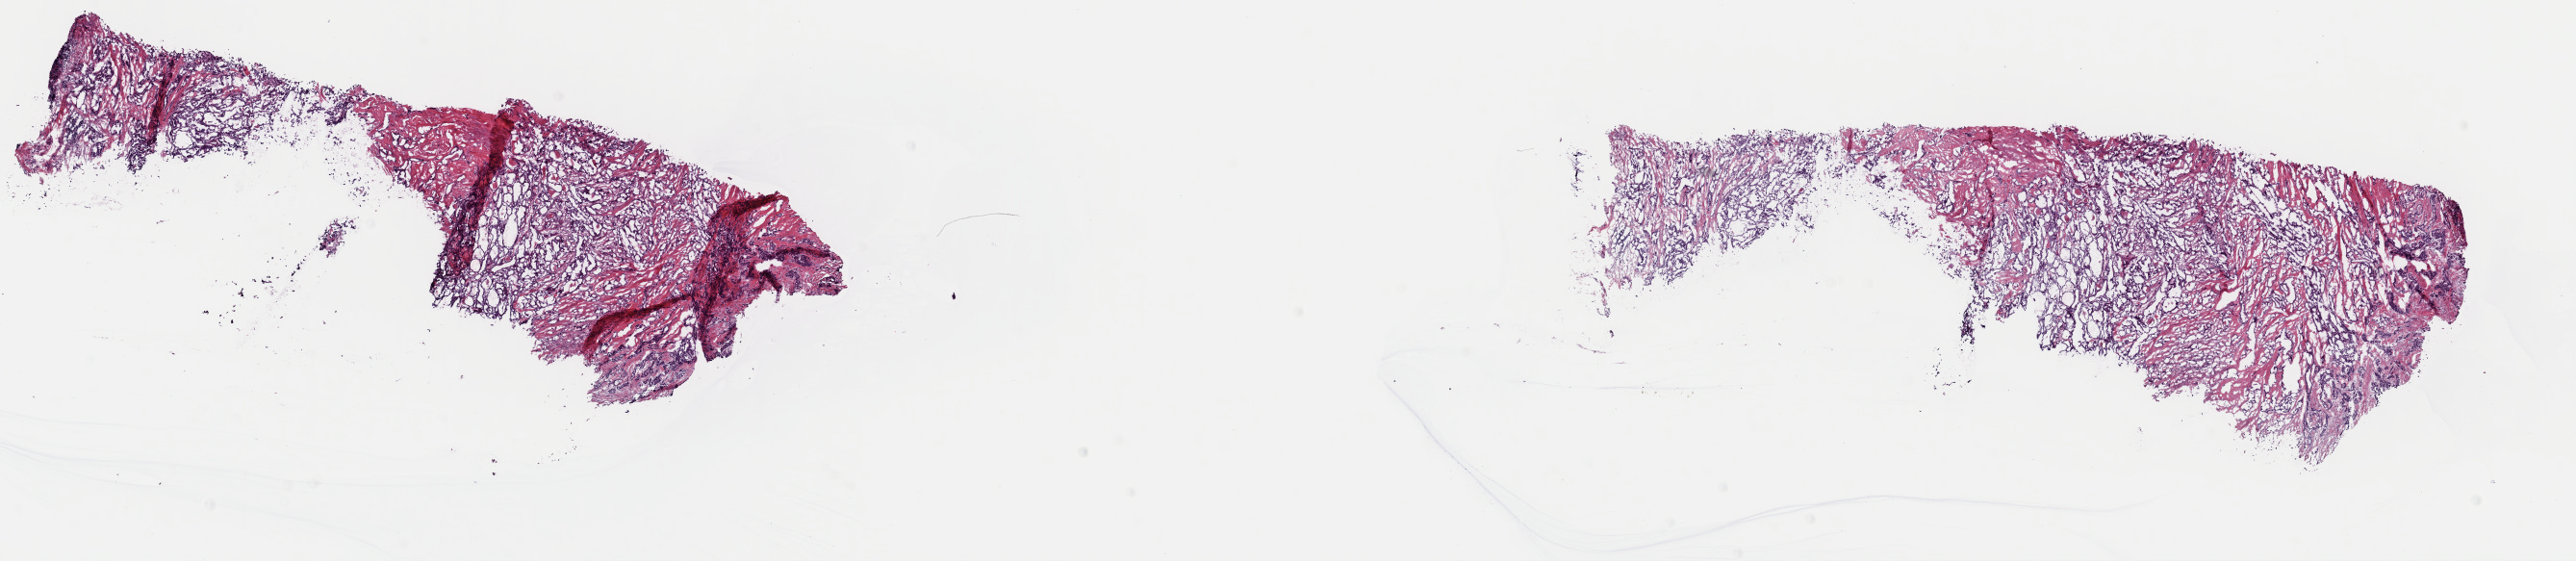
Digitized H&E-stained tissue section (whole slide) — low-resolution overview of the scanned area, about 21.1 x 4.6 mm; frozen section from the top of the tissue portion; thyroid, primary tumour sample. Patient: female, age at initial diagnosis 57 years. Slide review estimates, as recorded: tumour cells 45%, tumour nuclei 100%, normal cells 0%, stromal cells 55%, necrosis 0%. Inflammatory infiltration, as recorded: lymphocyte infiltration 1%, monocyte infiltration 1%, neutrophil infiltration 0%.
• pathologic diagnosis: Papillary adenocarcinoma, NOS (thyroid gland)
• AJCC pathologic stage: IVA (7th edition)